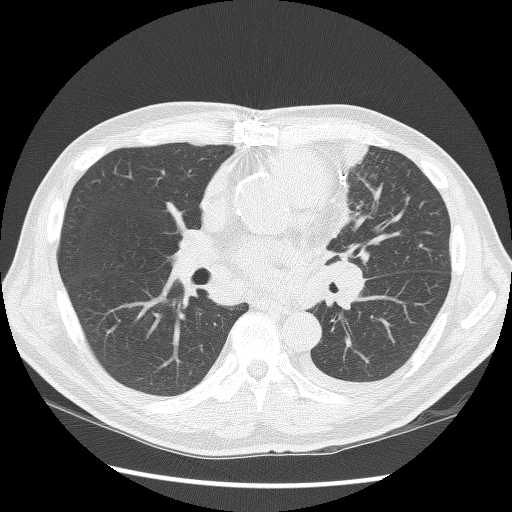
Chest CT (low-dose screening protocol), one axial image. Second annual screen. Lung window (W 1500 / L -600 HU). 2.5 mm slice thickness. Lung (sharp) reconstruction kernel (BONE). 120 kVp. Slice 62 of 136 in the series. Male participant, aged 64 years at enrolment. Former smoker at enrolment.
Expert-annotated lung lesion, bounding box [x1, y1, x2, y2] px = [307, 124, 398, 276]. No non-calcified nodule or mass ≥4 mm was recorded by the screening reader at this exam. Official screen result: positive, other. Participant outcome: lung cancer diagnosed 24 days after this screen — small cell carcinoma, NOS, left upper lobe, stage IV (AJCC 6th edition), 100 mm at pathology.